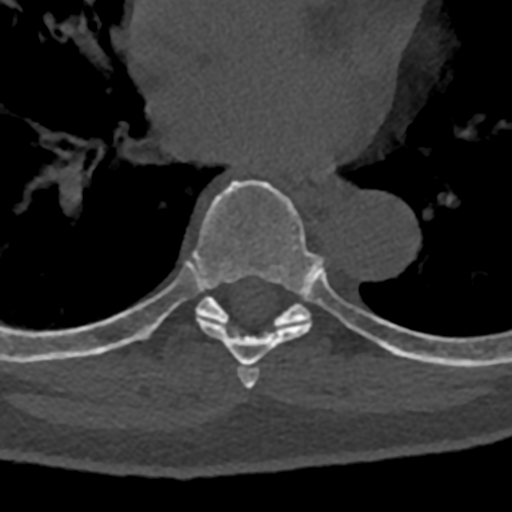
CT including the spine, one axial slice; slice 745 of 797 in the series (ordered by position); reconstruction kernel Br40s/3; bone window (W 1800 / L 400 HU); 0.5 mm slice thickness; 512 × 512 image matrix. Patient: male, 74 years. From the clinical record (not read from this slice): primary cancer: renal.
Annotated regions visible in this slice (semi-automatic segmentation, software-assisted and operator-edited):
- T6 vertebra: bounding box <238,366,259,389> (left, top, right, bottom; pixels)
- T7 vertebra: <71,180,394,369>
- T8 vertebra: <70,296,432,363>